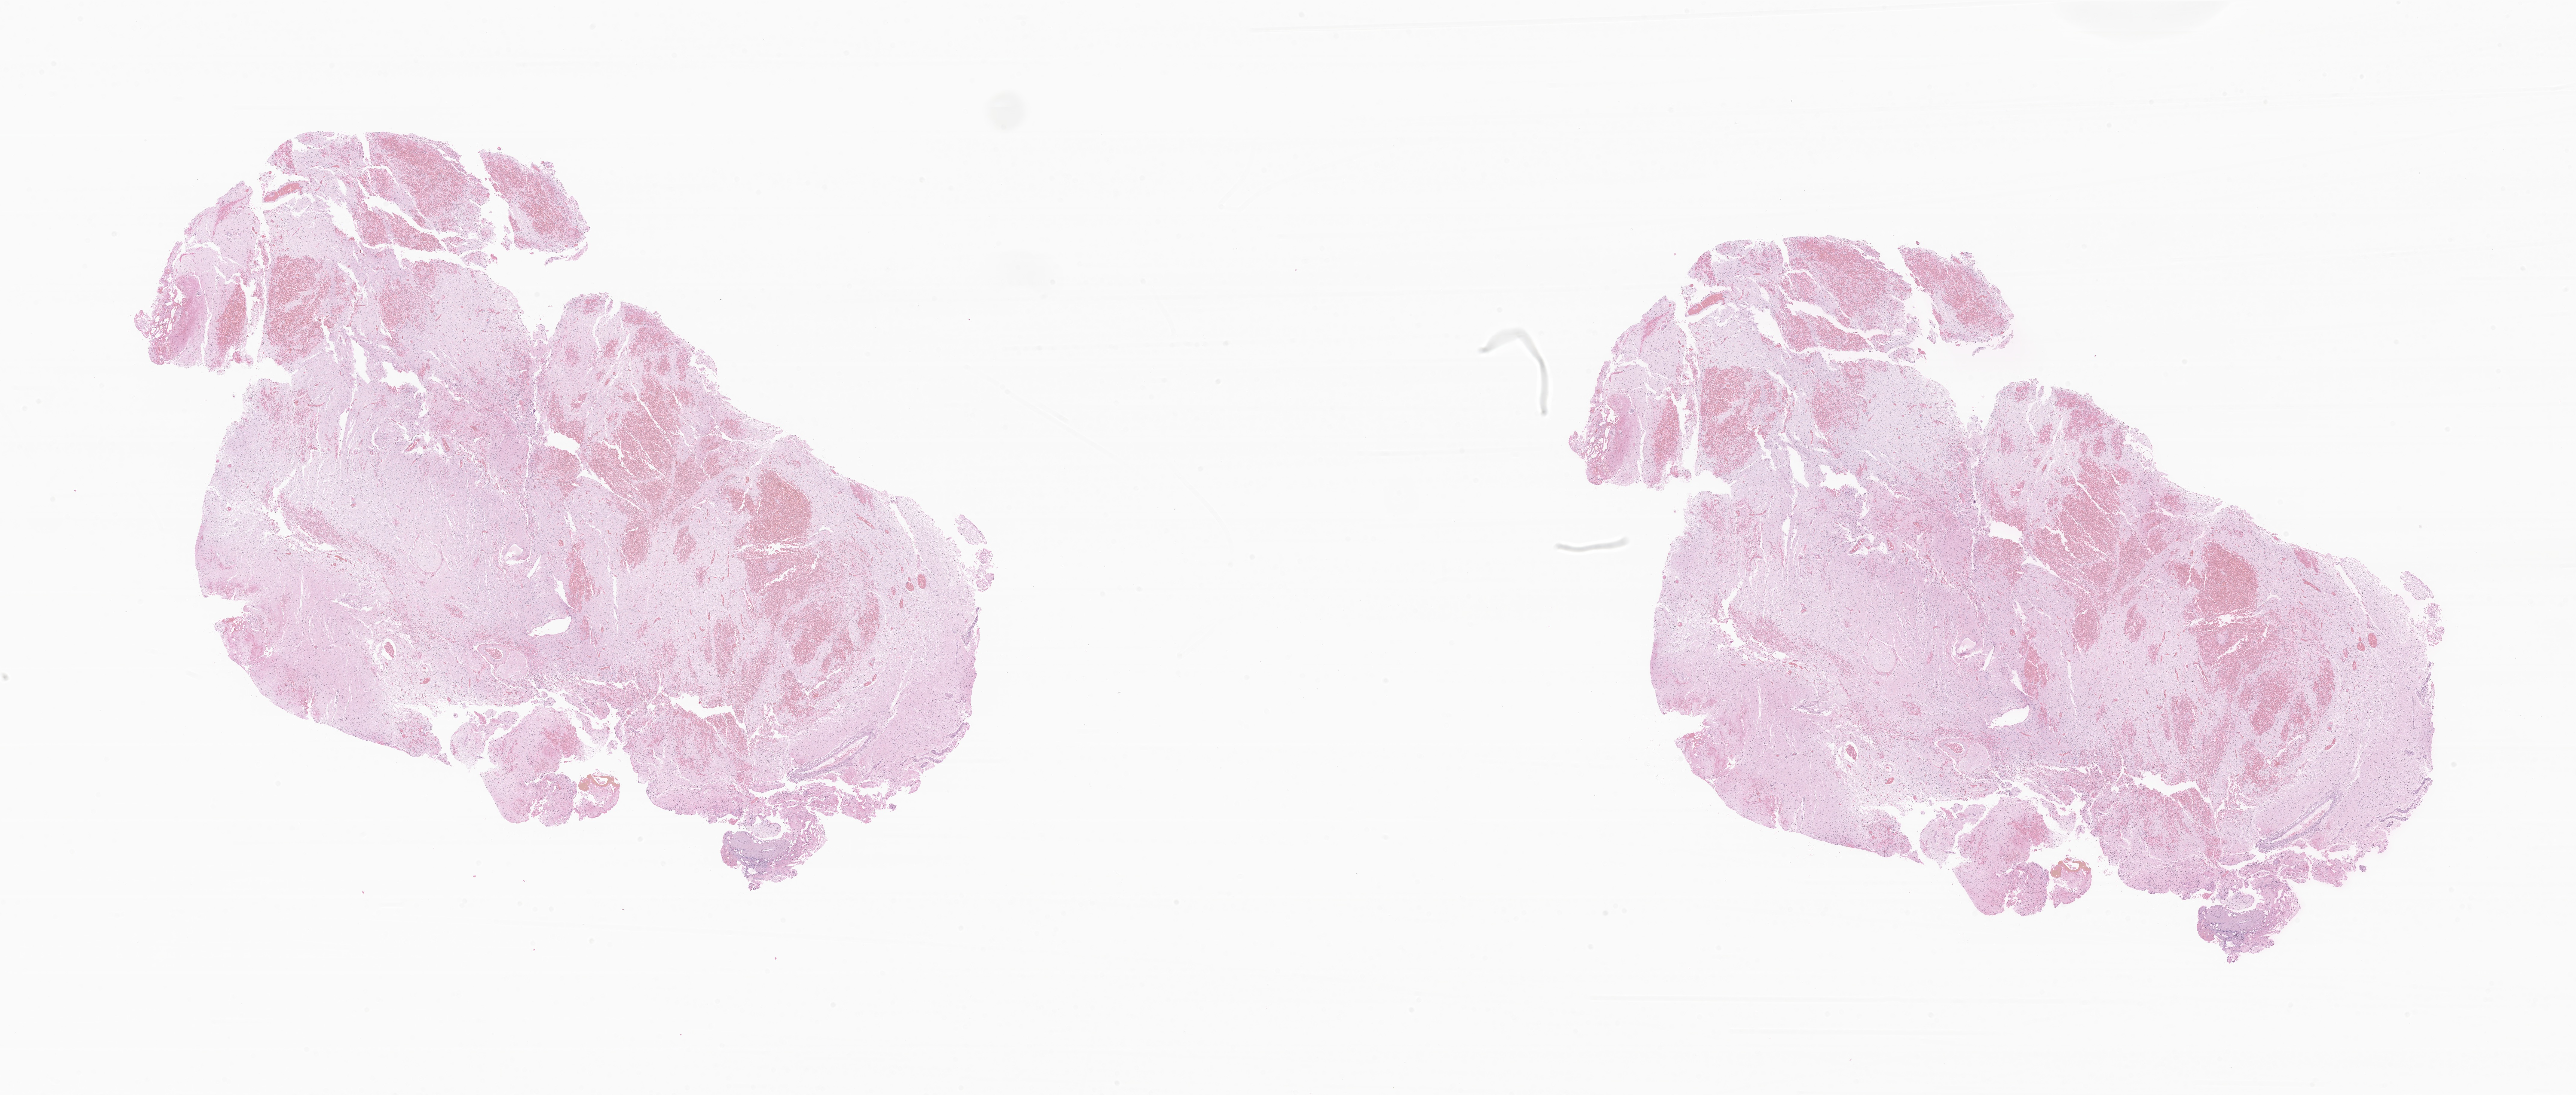
Haematoxylin and eosin whole-slide image of tumor tissue from the brain — low-resolution overview of the scanned area, about 36.1 x 15.4 mm. Formalin-fixed, paraffin-embedded (FFPE) tissue. Female patient, age 110 months (9 years 2 months).
Diagnosis: Pilocytic astrocytoma.